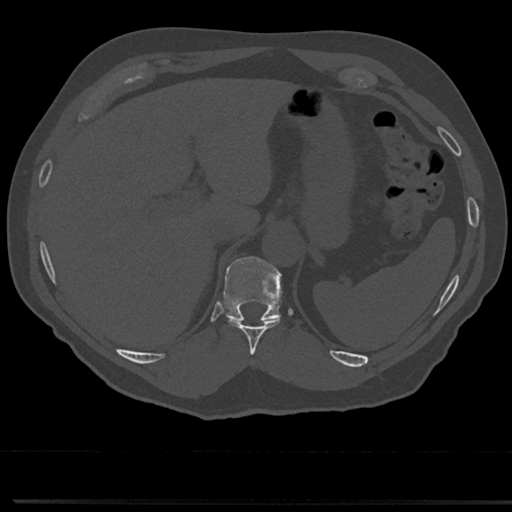
CT including the spine, one axial slice. Slice 231 of 817 in the series (ordered by position). Reconstruction kernel Br40s/3. 120 kVp. Bone window (W 1800 / L 400 HU). 0.5 mm slice thickness. 512 × 512 image matrix, field of view 355 × 355 mm. Patient: male, 61 years. Case-level facts recorded for this patient, not image findings: primary cancer: prostate.
Annotated regions visible in this slice (semi-automatically segmented with operator editing):
- T10 vertebra: bounding box (x1, y1, x2, y2) in pixels: (226, 317, 282, 353)
- T11 vertebra: (224, 257, 281, 322)